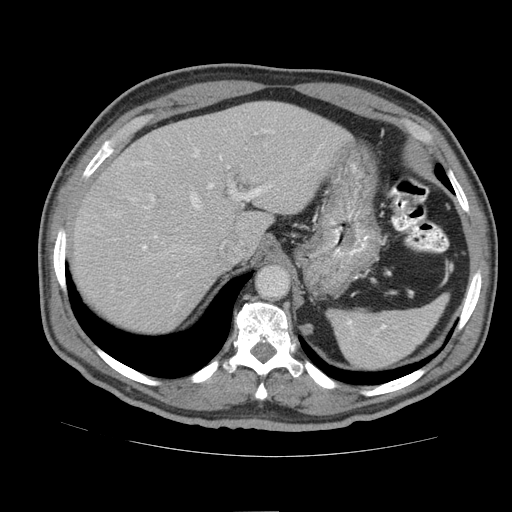
Contrast-enhanced abdominal CT (liver protocol), one axial slice; slice 65 of 105 in the series (ordered by position); soft-tissue window (W 400 / L 40 HU); 2.5 mm slice thickness; 512 × 512 image matrix, field of view 380 × 380 mm. Case-level facts recorded for this patient, not image findings: diagnosis: hepatocellular carcinoma (patient treated with transarterial chemoembolisation; whether this scan precedes or follows treatment is not stated here); TNM stage (as recorded): Stage-IIIB; Child-Pugh class: A; tumour nodularity: multinodular.
Outlined on this slice (semi-automatically segmented with operator editing):
- liver parenchyma outside the tumour (the mass and vessels are separate outlines, so this box may not span the whole liver): bounding box (x1, y1, x2, y2) in pixels: (70, 102, 352, 330)
- liver vessels: (142, 130, 271, 250)